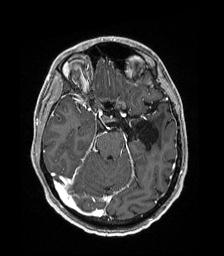
Brain MRI from a brain-tumour surgery series, one axial slice. Slice 116 of 192 in the series (ordered by position). T1-weighted post-contrast. 1 mm slice thickness. 224 × 256 image matrix. From the clinical record (not read from this slice): histopathology: Low grade glioma; IDH mutation: no; tumour location: Left Parieto-Occipital Intraventricular.
Outlined on this slice (manually delineated by an expert):
- previous resection cavity: bounding box <135,120,159,151> (left, top, right, bottom; pixels)